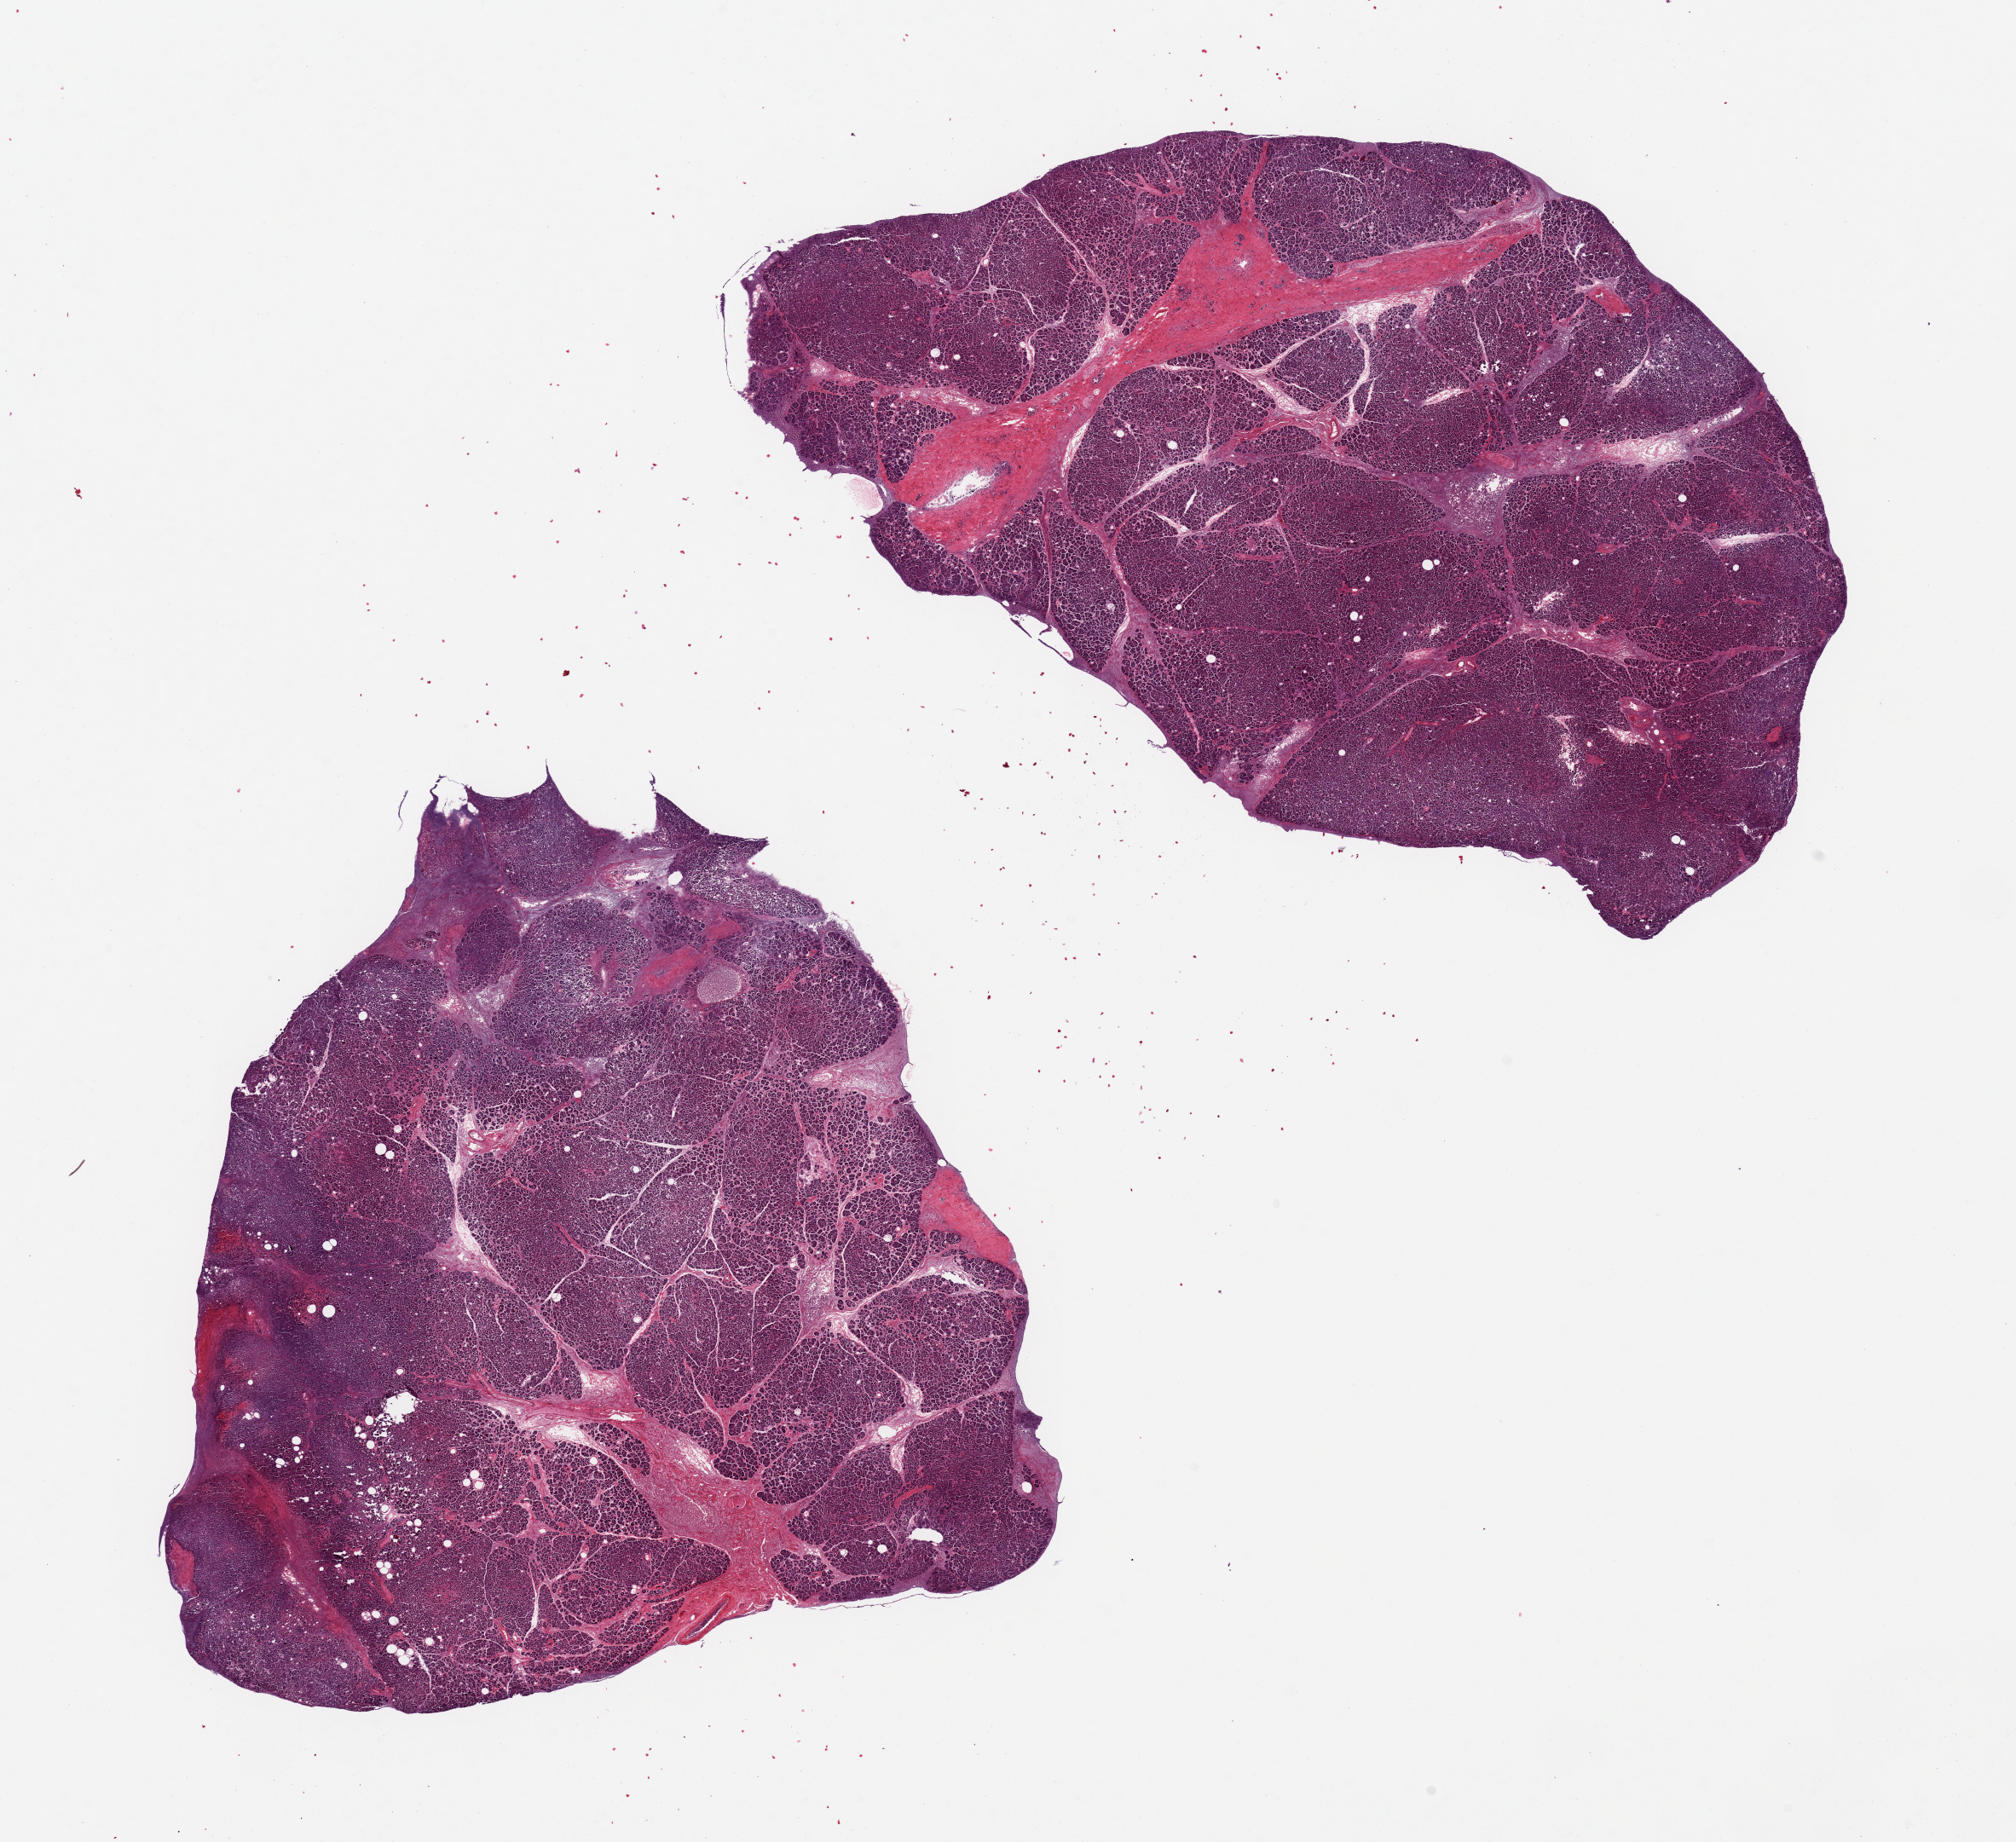
Digitized haematoxylin and eosin-stained section — whole scanned area (about 18.7 x 17.1 mm, acquisition: 20x scan) shown as a low-resolution overview. PAXgene-fixed paraffin-embedded (PFPE) section. Target tissue: pancreas. Tissue donor sample. Donor sex: male.
Reviewer comment on this tissue sample: 2 pieces 10x6 & 8x8 mm.